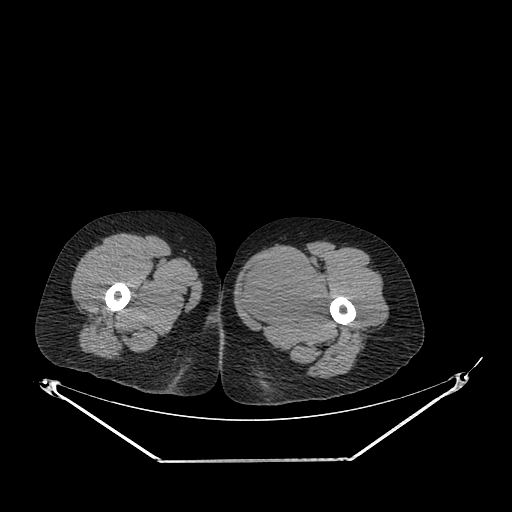
CT of an extremity soft-tissue mass (from a PET/CT study), one axial slice; slice 243 of 267 in the series (ordered by position); reconstruction kernel SOFT; 120 kVp; soft-tissue window (W 400 / L 40 HU); 3.75 mm slice thickness; 512 × 512 image matrix, field of view 500 × 500 mm. Female patient. From the clinical record (not read from this slice): histological type: pleiomorphic leiomyosarcoma; grade: intermediate; site of the primary tumour: left thigh.
Annotated regions visible in this slice (expert contour drawn on MRI and transferred to this co-registered scan by the dataset authors):
- gross tumour volume including surrounding oedema: bounding box [x1, y1, x2, y2] px = [238, 260, 328, 328]
- gross tumour volume (mass): [238, 260, 328, 328]